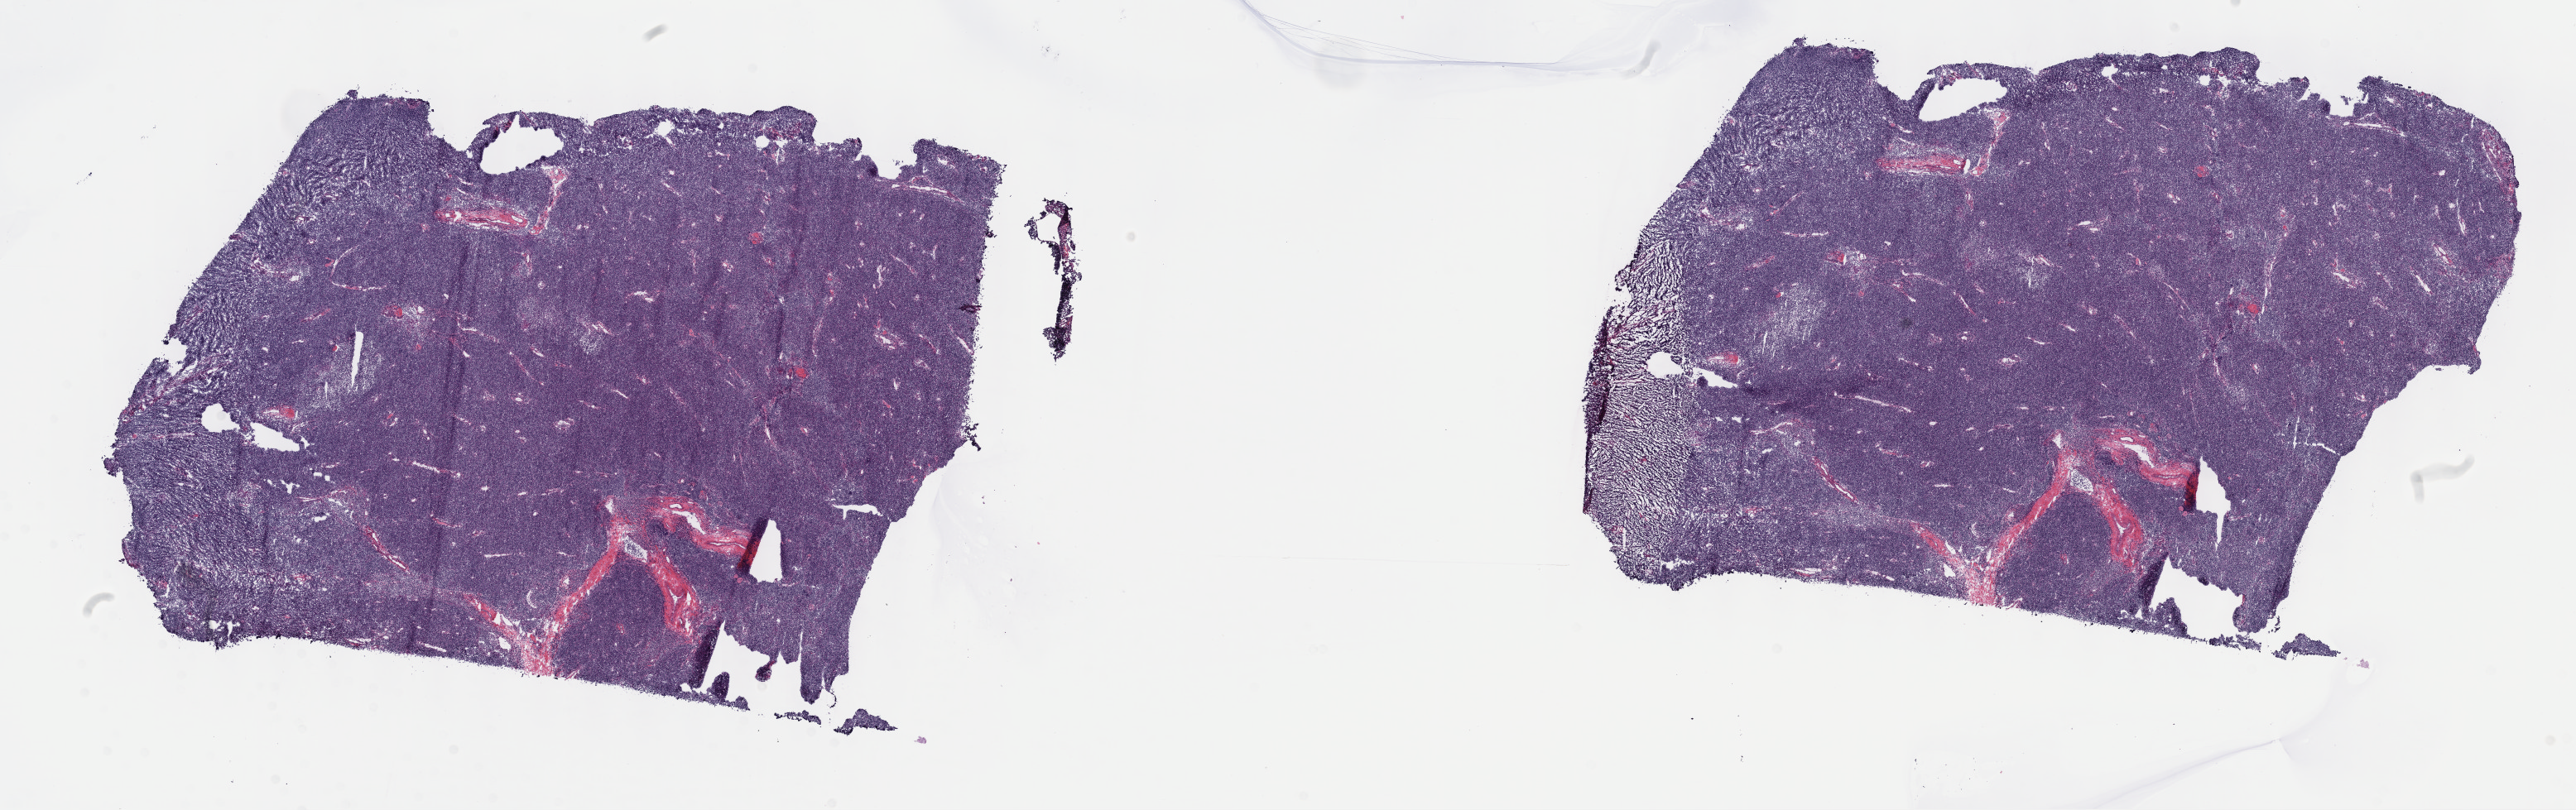
Whole-slide histology image, Hematoxylin and eosin (H&E) stained, shown as a low-resolution overview of the whole scanned area (about 25.2 x 7.9 mm, from a 40x scan), frozen section, sample: primary tumour, thymus. Male, age 38 years at initial diagnosis. Slide review estimates, as recorded: tumour cells 100%, tumour nuclei 80%.
Diagnosis: Thymoma, type B2, malignant.